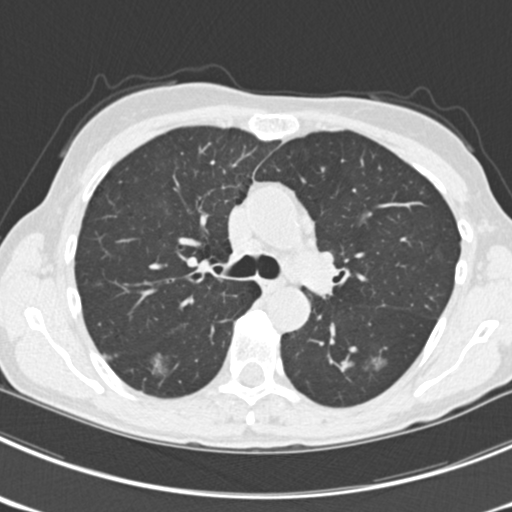
Axial slice from a low-dose chest CT screening exam. Third screening round (two years after baseline). Lung window (W 1500 / L -600 HU). Standard (soft-tissue) reconstruction kernel (B30f). 512 × 512 image matrix, field of view 302 × 302 mm. Female participant, aged 63 years at enrolment. Current smoker at enrolment.
2 expert reader's lesion annotations on this slice (largest first), bounding box (x1, y1, x2, y2) in pixels: (139, 342, 180, 384); (356, 346, 398, 382). The screening reader recorded 9 non-calcified nodules or masses ≥4 mm on this exam (left upper lobe, right upper lobe, left upper lobe, left lower lobe, right middle lobe, left lower lobe, left lower lobe, right lower lobe, right lower lobe); which of them these boxes mark is not recorded. Official screen result: positive, other.